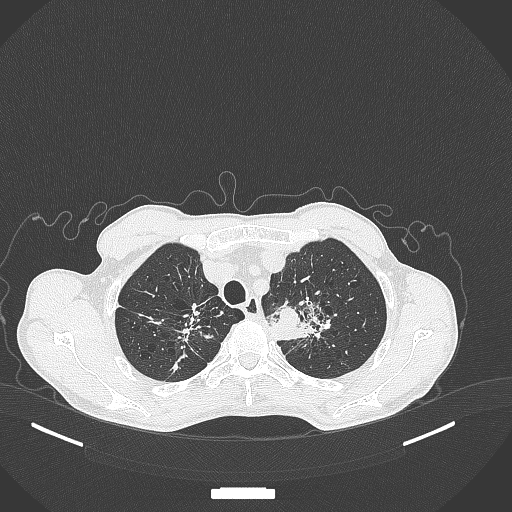
Chest CT, one axial slice; position 359 of 386 along the scan axis; lung window (W 1500 / L -600 HU); 1 mm slice thickness; 512 × 512 image matrix, field of view 400 × 400 mm. Patient: male, 65 years. From the clinical record (not read from this slice): clinical TNM (as recorded): T2b N0 M0; histopathological grade: G2.
Structures marked on this image (bounding box drawn by a radiologist):
- lung tumour (recorded histology: adenocarcinoma): box from (x=268, y=294) to (x=306, y=329) px